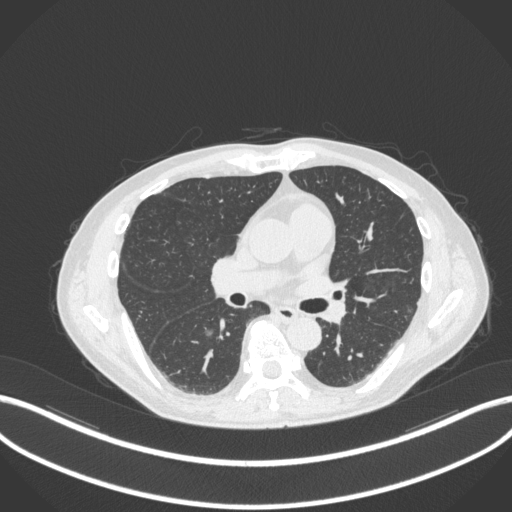
Chest CT, one axial slice. Position 176 of 324 along the scan axis. Reconstruction kernel B31f. 120 kVp. Lung window (W 1500 / L -600 HU). 1 mm slice thickness. 512 × 512 image matrix, field of view 400 × 400 mm. Male patient, age 61 years. From the clinical record (not read from this slice): clinical TNM (as recorded): T1c N0 M0.
Annotated regions visible in this slice (bounding box drawn by a radiologist):
- lung tumour (recorded histology: adenocarcinoma): bounding box [x1, y1, x2, y2] px = [200, 325, 219, 340]